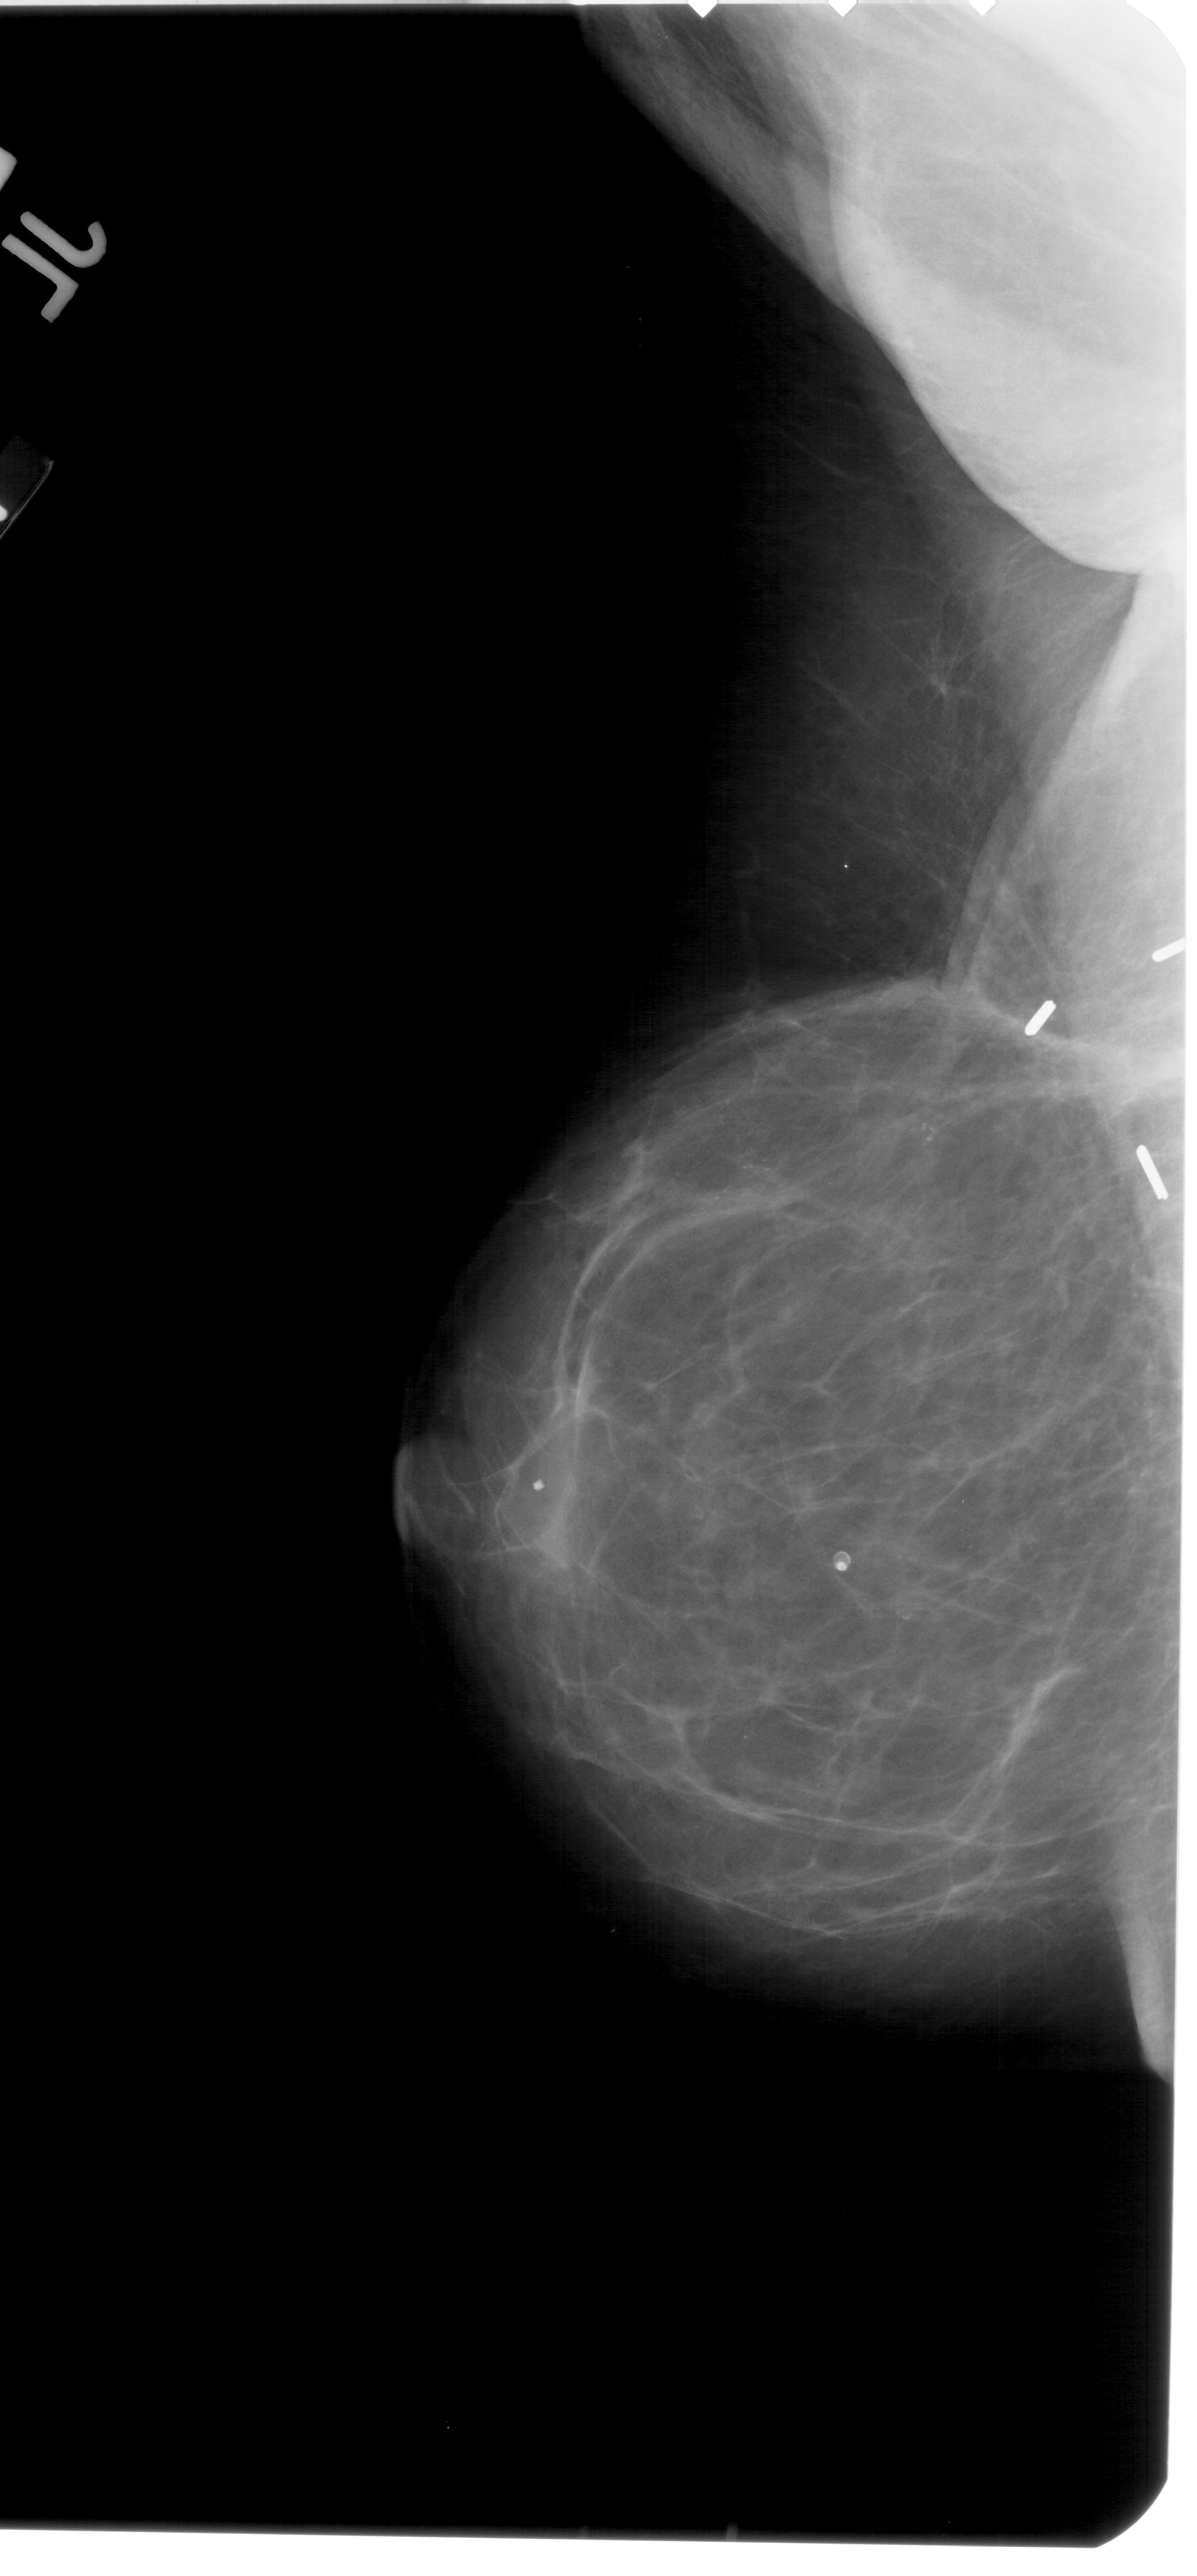
Scanned film-screen mammogram. Left breast. Mediolateral oblique (MLO) view. BI-RADS breast density category 3 (scale 1–4). 1197 × 2576 image matrix.
Expert-marked regions of interest on this film, with their recorded descriptors:
- calcifications, morphology pleomorphic, distribution linear; BI-RADS assessment category 5; pathology (as recorded): malignant: box from (x=557, y=1022) to (x=1009, y=1320) px